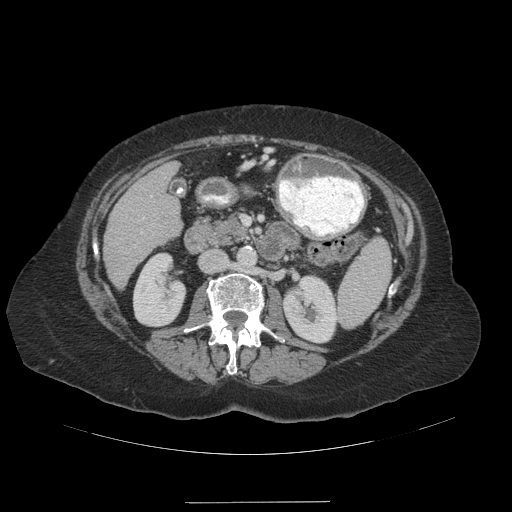
Contrast-enhanced abdominal CT (liver protocol), one axial slice. Position 46 of 99 along the scan axis. Reconstruction kernel STANDARD. 140 kVp. Soft-tissue window (W 400 / L 40 HU). 512 × 512 image matrix, field of view 440 × 440 mm. From the clinical record (not read from this slice): diagnosis: hepatocellular carcinoma (patient treated with transarterial chemoembolisation; whether this scan precedes or follows treatment is not stated here); TNM stage (as recorded): Stage-IVA; Child-Pugh class: A.
Outlined on this slice (semi-automatically segmented with operator editing):
- liver parenchyma outside the tumour (the mass and vessels are separate outlines, so this box may not span the whole liver): bounding box (x1, y1, x2, y2) in pixels: (102, 162, 182, 288)